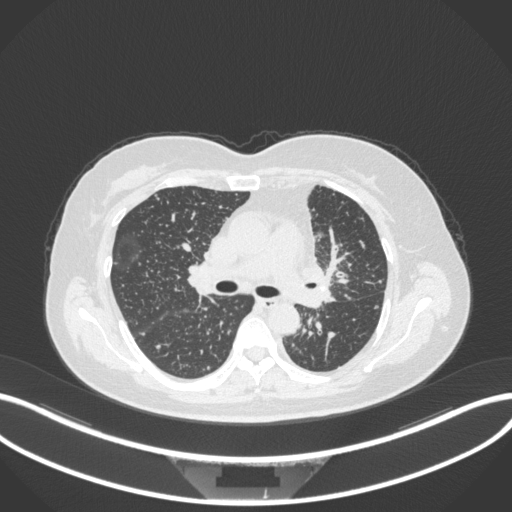
Chest CT, one axial slice. Position 205 of 348 along the scan axis. Reconstruction kernel B31f. Lung window (W 1500 / L -600 HU). 1 mm slice thickness. 512 × 512 image matrix. Patient: female, 49 years. From the clinical record (not read from this slice): clinical TNM (as recorded): T1c N0 M1.
Annotated regions visible in this slice (rectangle marked by the reading radiologist):
- lung tumour (recorded histology: adenocarcinoma): box from (x=293, y=256) to (x=342, y=310) px